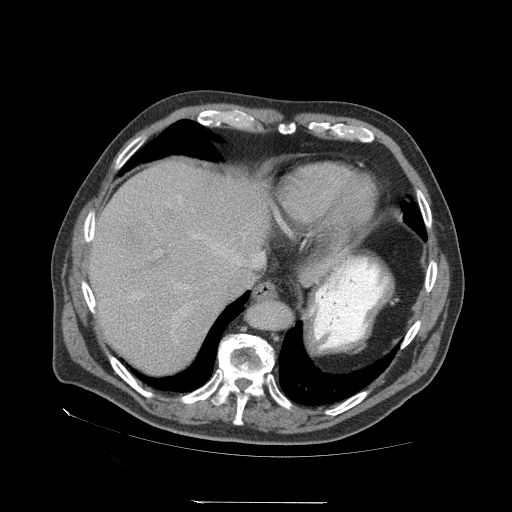
Contrast-enhanced abdominal CT (liver protocol), one axial slice; slice 57 of 83 in the series (ordered by position); reconstruction kernel STANDARD; soft-tissue window (W 400 / L 40 HU); 2.5 mm slice thickness; 512 × 512 image matrix, field of view 460 × 460 mm. From the clinical record (not read from this slice): diagnosis: hepatocellular carcinoma (patient treated with transarterial chemoembolisation; whether this scan precedes or follows treatment is not stated here); TNM stage (as recorded): Stage-I; Child-Pugh class: A; tumour differentiation: well differentiated.
Annotated regions visible in this slice (semi-automatically segmented with operator editing):
- abdominal aorta: box from (x=251, y=302) to (x=292, y=330) px
- liver parenchyma outside the tumour (the mass and vessels are separate outlines, so this box may not span the whole liver): (x=88, y=160)–(x=269, y=374)
- liver vessels: (x=133, y=197)–(x=263, y=320)